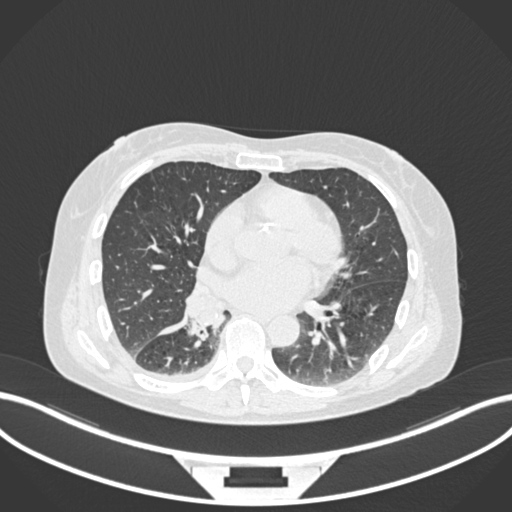
Chest CT, one axial slice. Slice 73 of 168 in the series (ordered by position). Reconstruction kernel B30f. Lung window (W 1500 / L -600 HU). 512 × 512 image matrix. Female patient, age 63 years. From the clinical record (not read from this slice): clinical TNM (as recorded): T1c N0 M0.
Outlined on this slice (rectangle marked by the reading radiologist):
- lung tumour (recorded histology: adenocarcinoma): bounding box (x1, y1, x2, y2) in pixels: (187, 280, 233, 343)